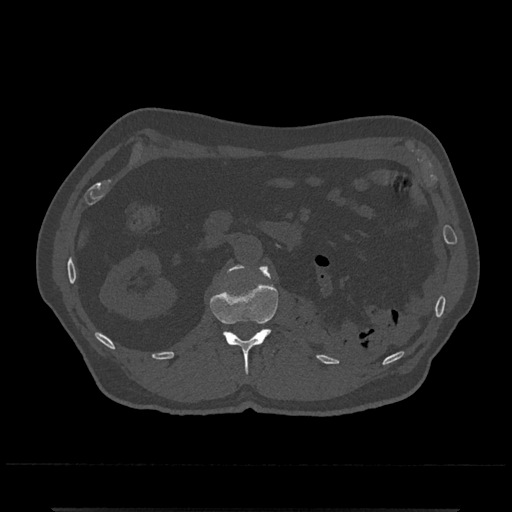
CT including the spine, one axial slice; reconstruction kernel Br40s/3; bone window (W 1800 / L 400 HU); 0.5 mm slice thickness; 512 × 512 image matrix. Male patient, age 67 years. Case-level facts recorded for this patient, not image findings: primary cancer: prostate.
Annotated regions visible in this slice (semi-automatic segmentation, software-assisted and operator-edited):
- L1 vertebra: bounding box <210,265,279,375> (left, top, right, bottom; pixels)